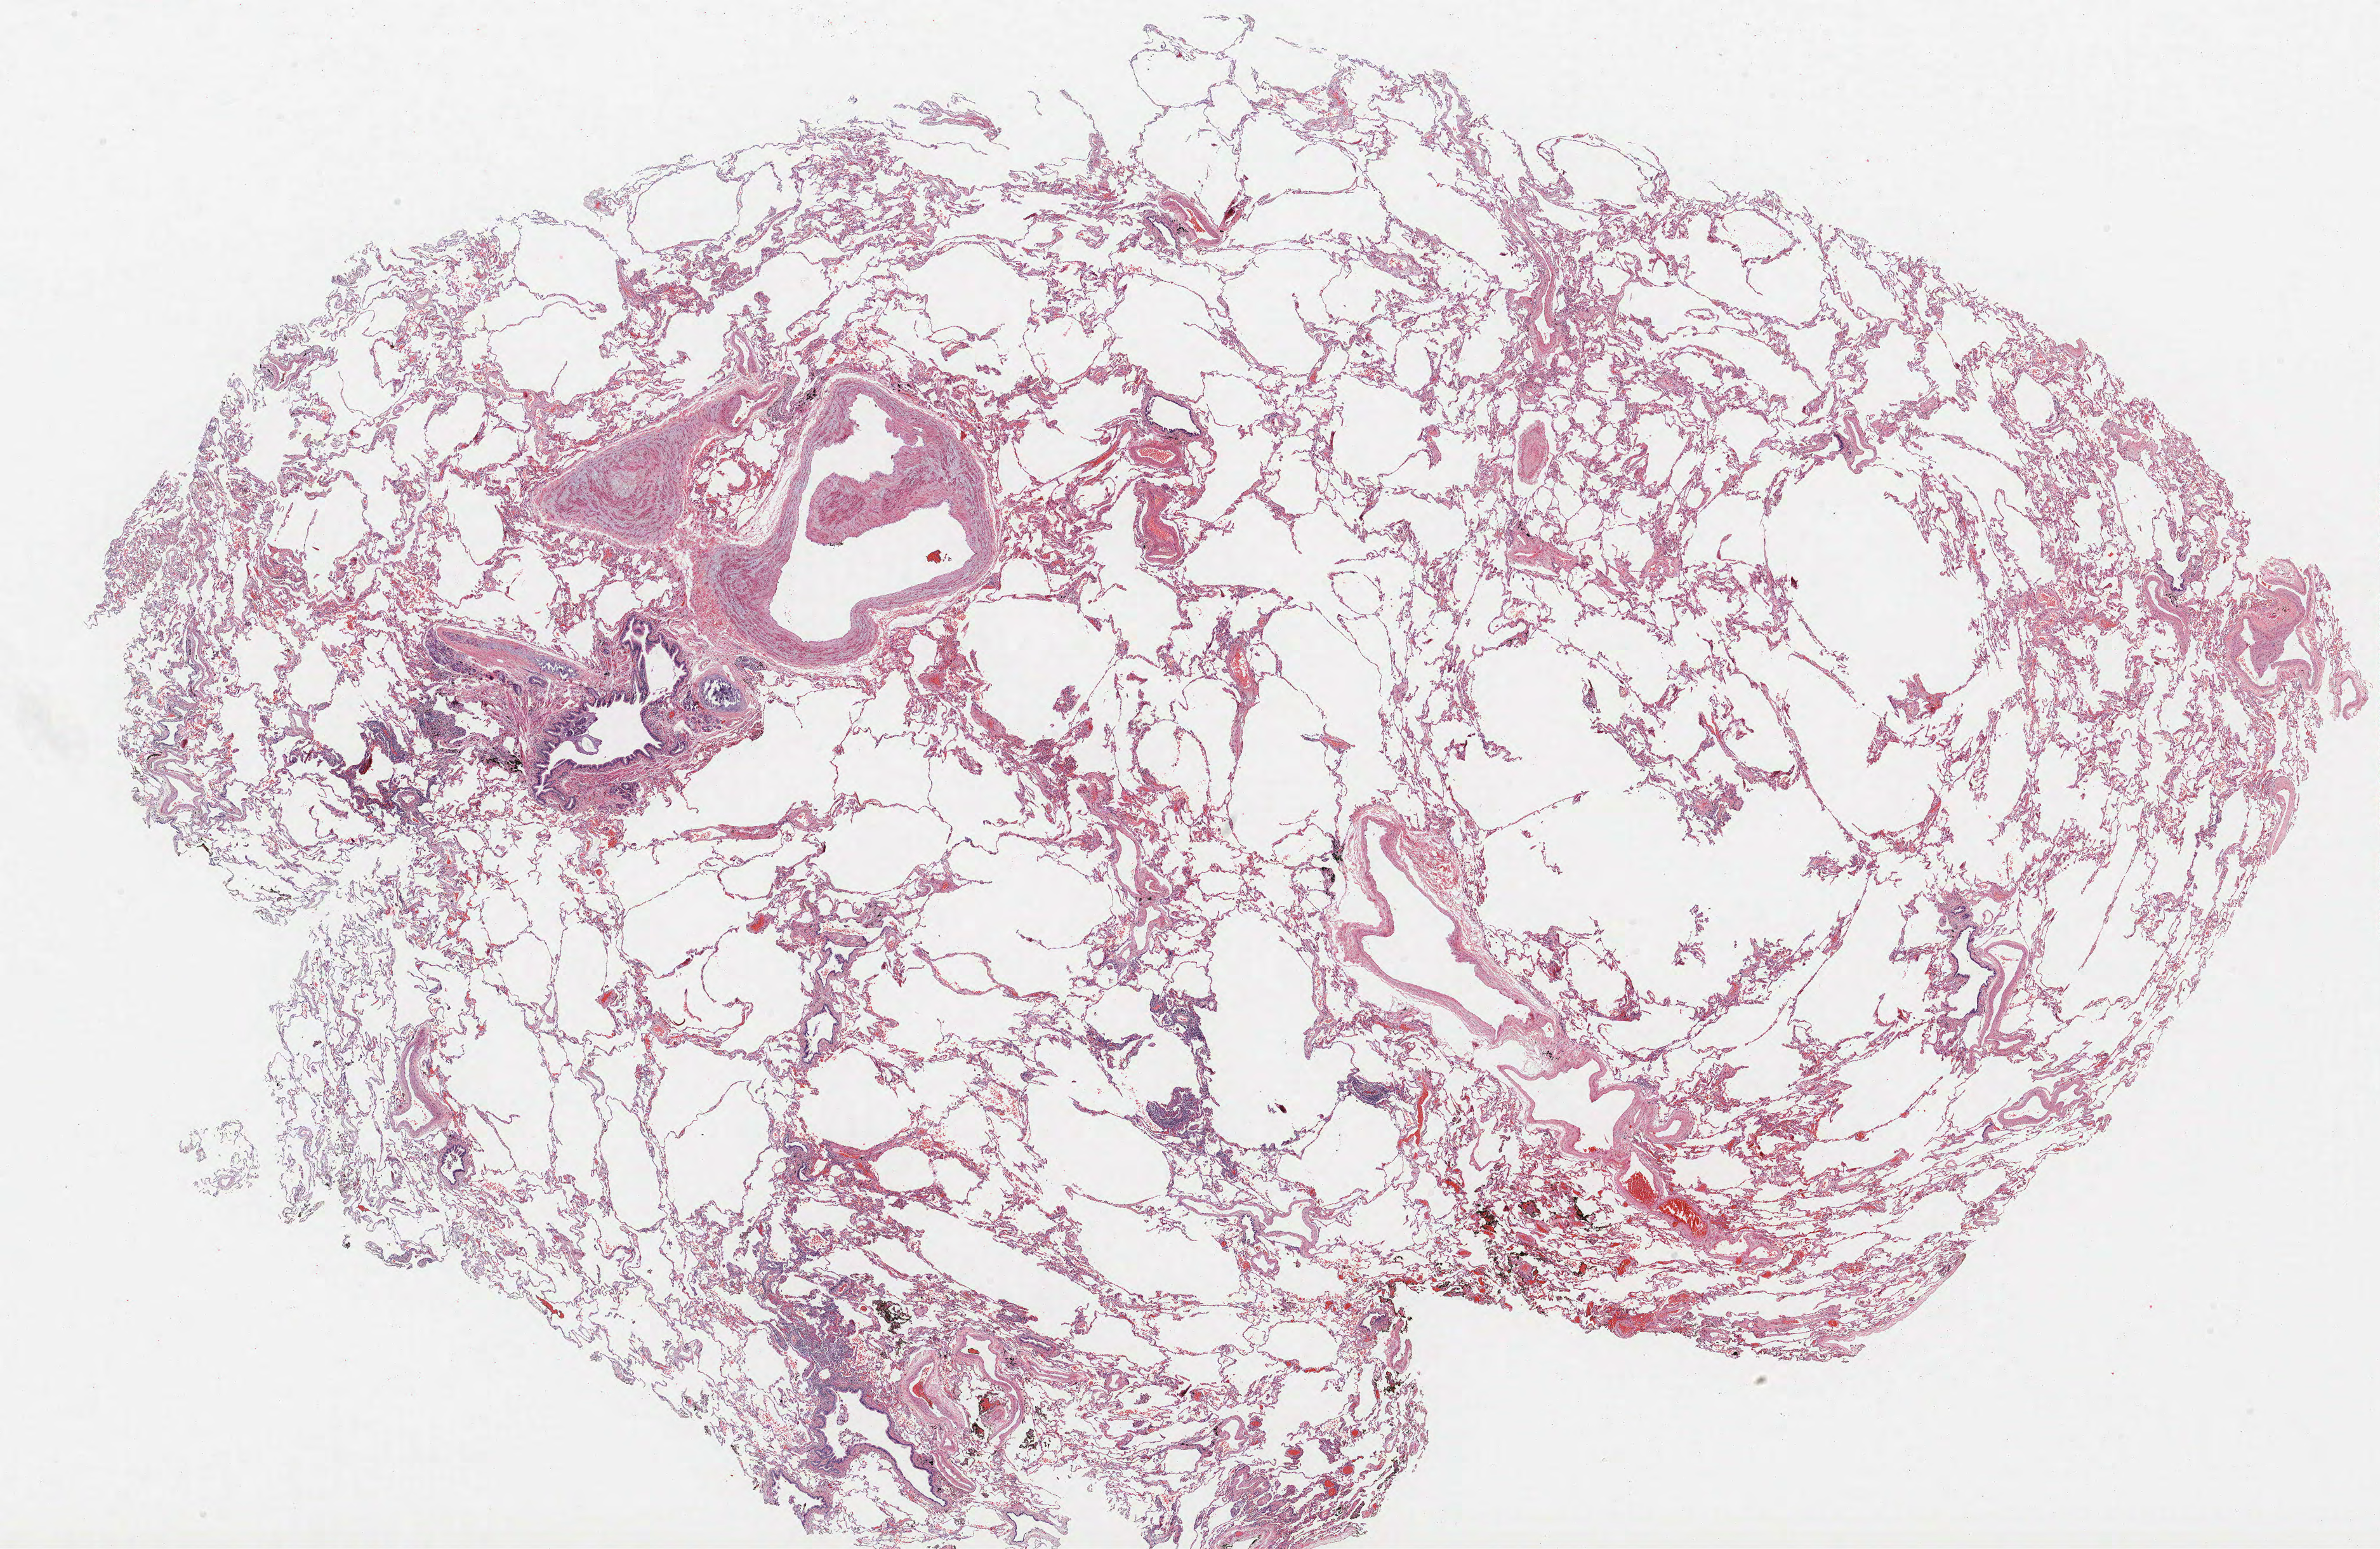
Whole-slide histology image, H&E-stained, whole scanned area (about 30.0 x 19.5 mm) shown as a low-resolution overview. FFPE section. Lung tissue. Female patient, aged 73 at enrolment. Current smoker at enrolment. Grade: moderately differentiated (G2).
- primary tumour location (clinical record): left upper lobe
- stage (AJCC 6th edition): IIIB
- participant's lung-cancer diagnosis: Bronchiolo-alveolar adenocarcinoma, NOS
- tumour size (pathology): 17 mm